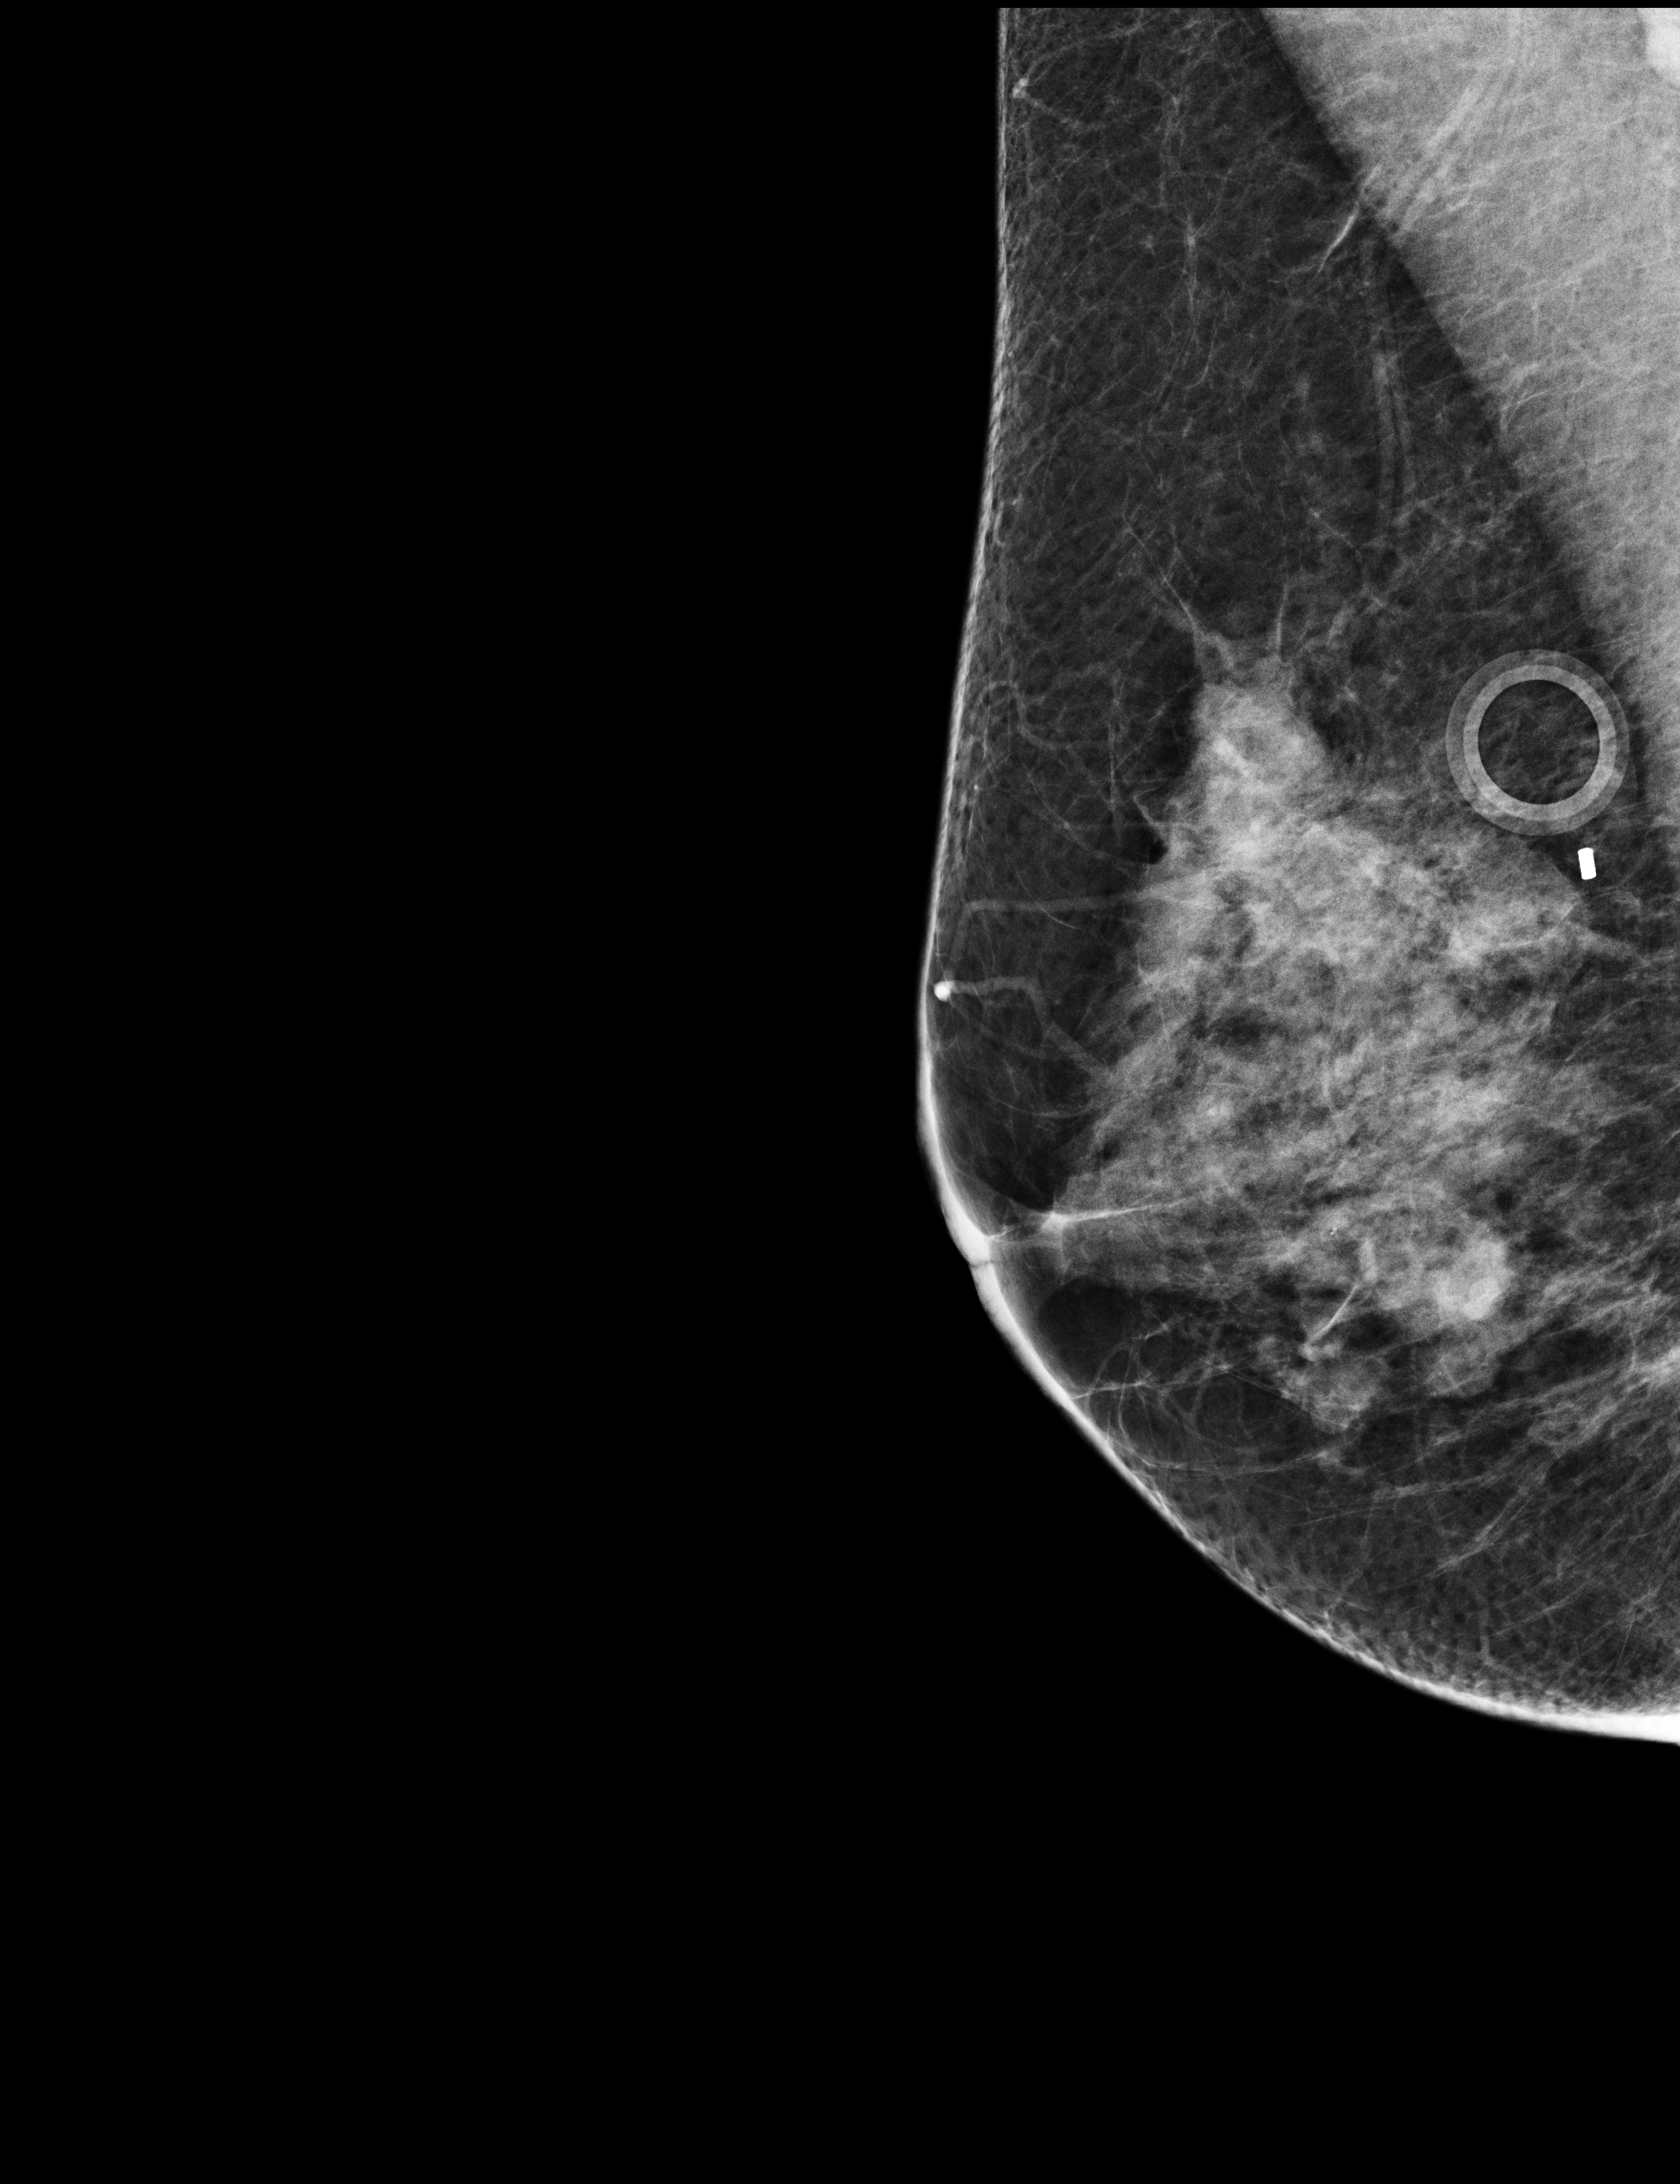
Annual screening mammography examination. Patient aged 59 years (female).
Image type: full-field digital mammogram. Breast: right. Projection: mediolateral oblique (MLO) view.